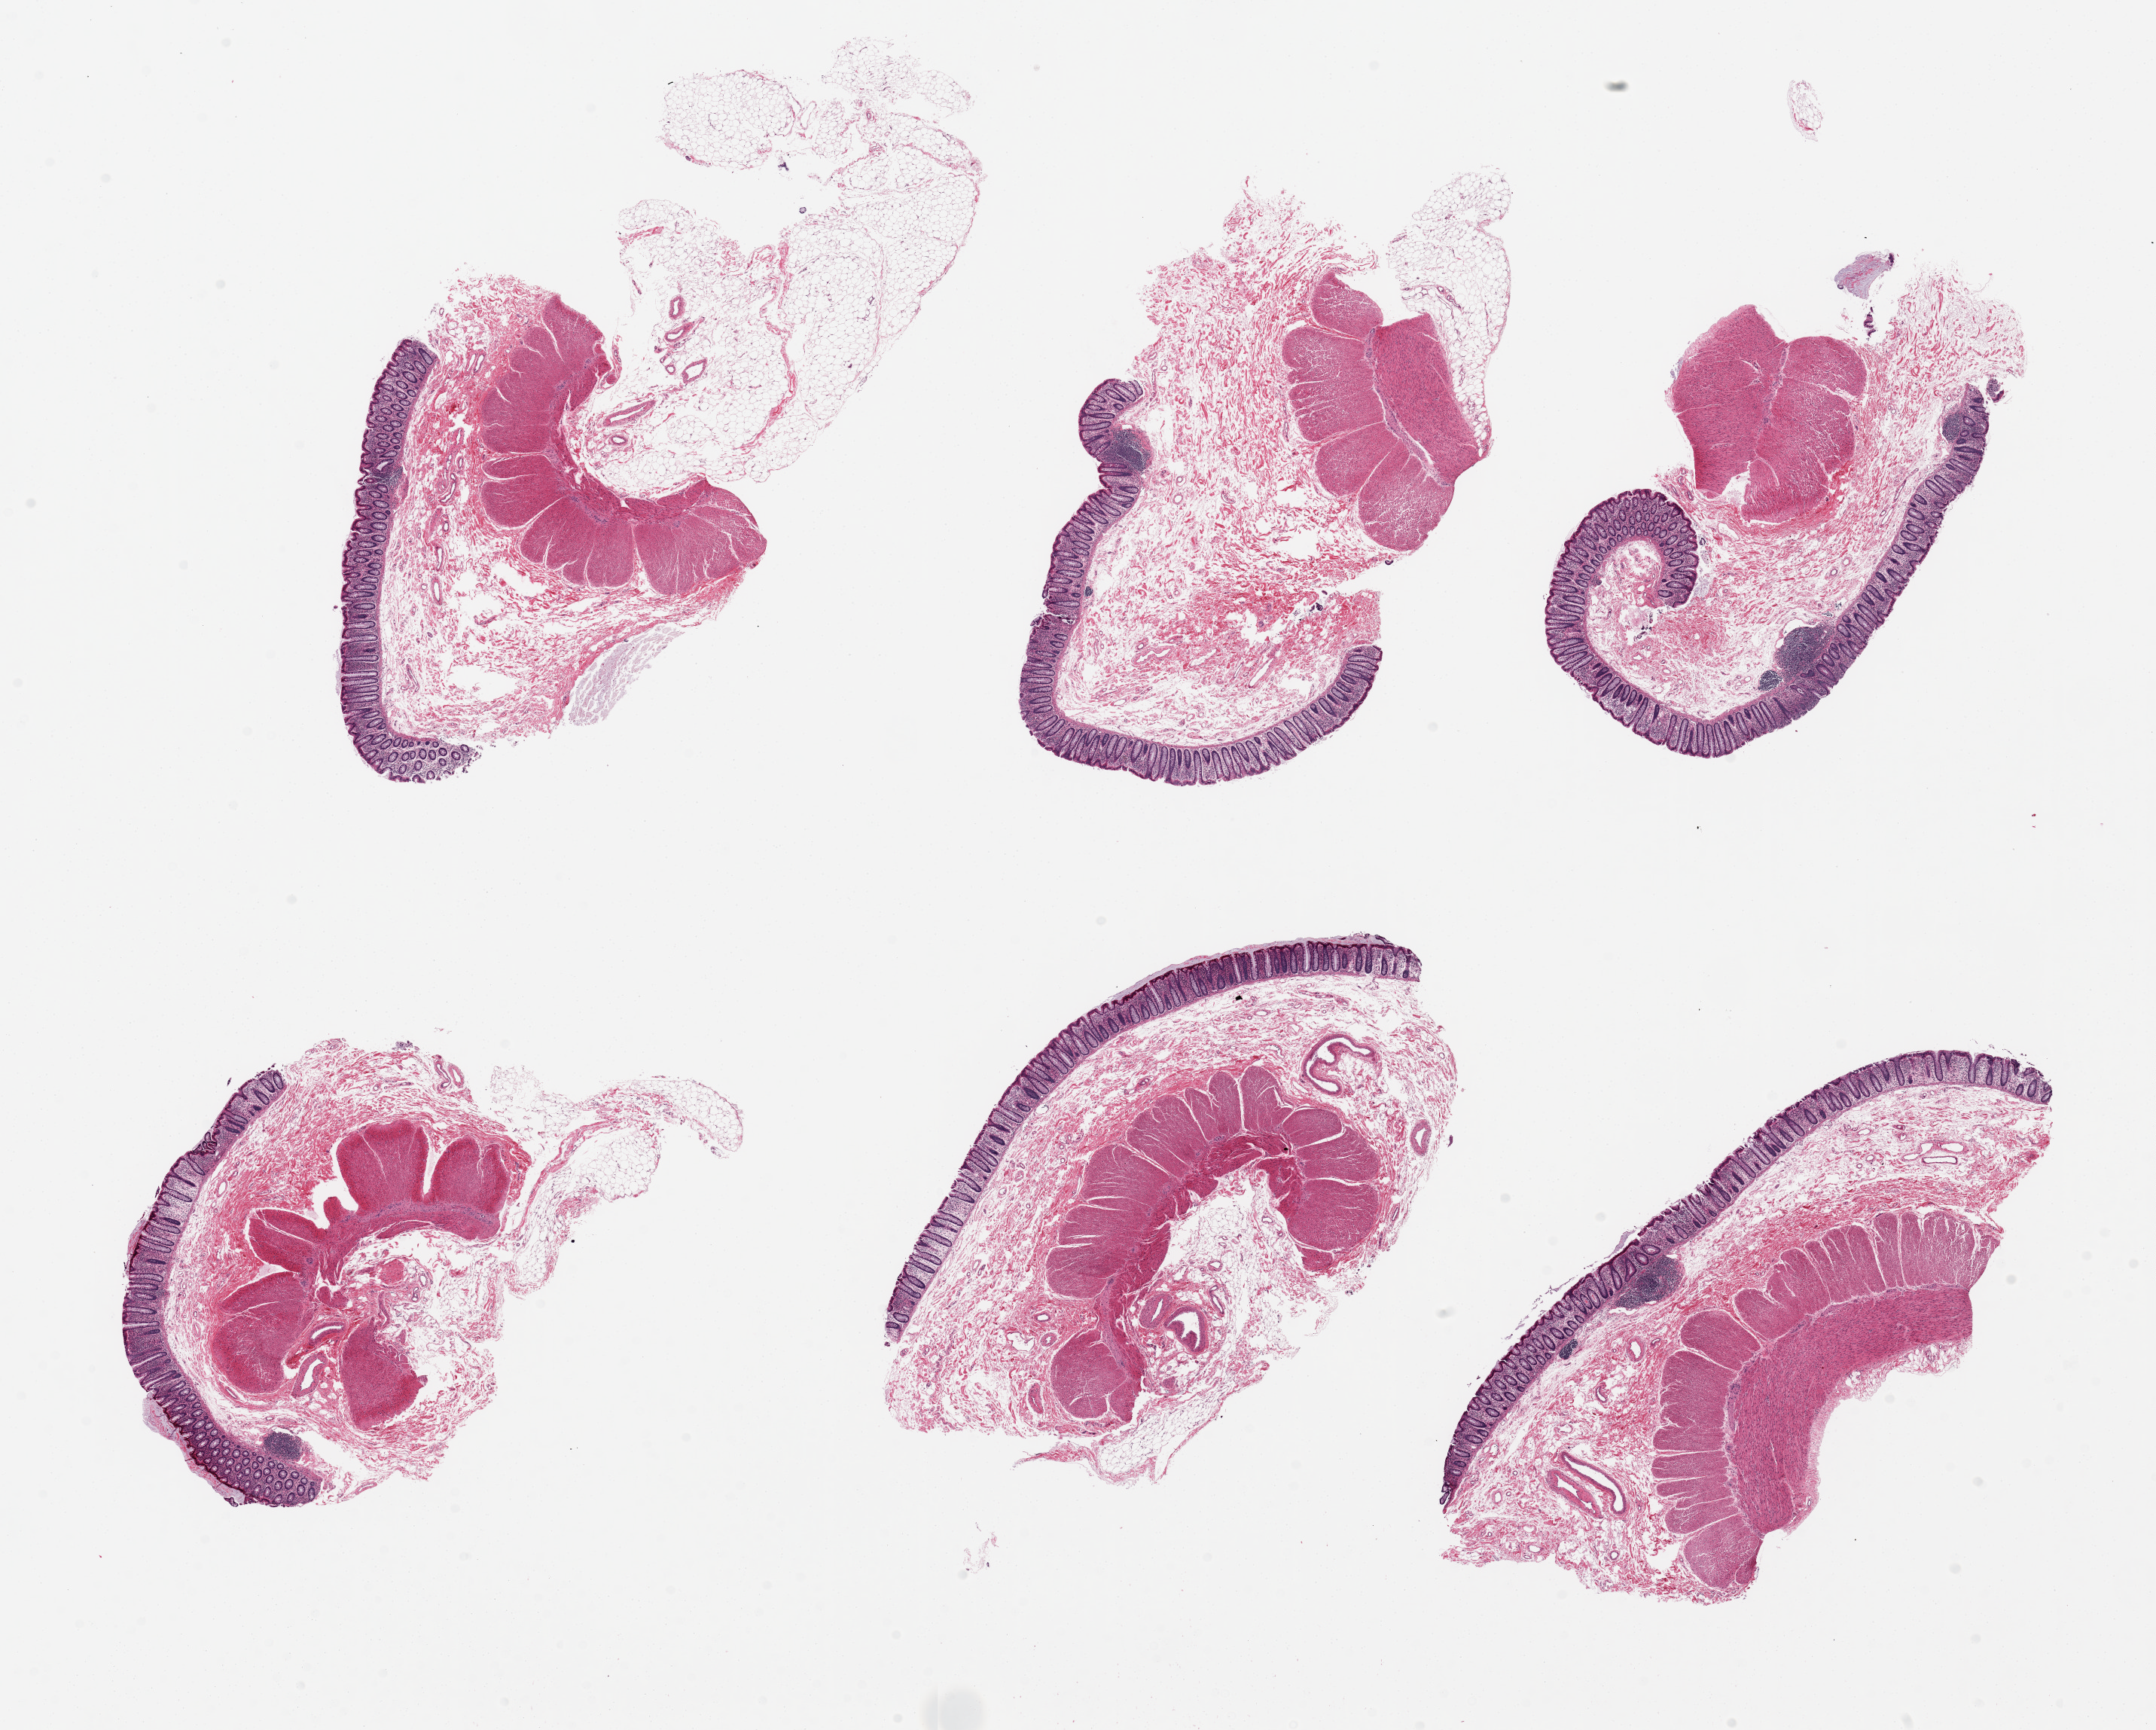
Haematoxylin and eosin whole-slide image — shown as a low-resolution overview of the whole scanned area (about 22.6 x 18.2 mm, slide scanned at 20x); PAXgene-fixed, paraffin-embedded tissue; section of transverse colon (target tissue); donor tissue sample. Female donor.
Review note (as recorded): 6 pieces, up to 9.5x4mm; mucosa well preserved, mucosa ~5-10% thickness.